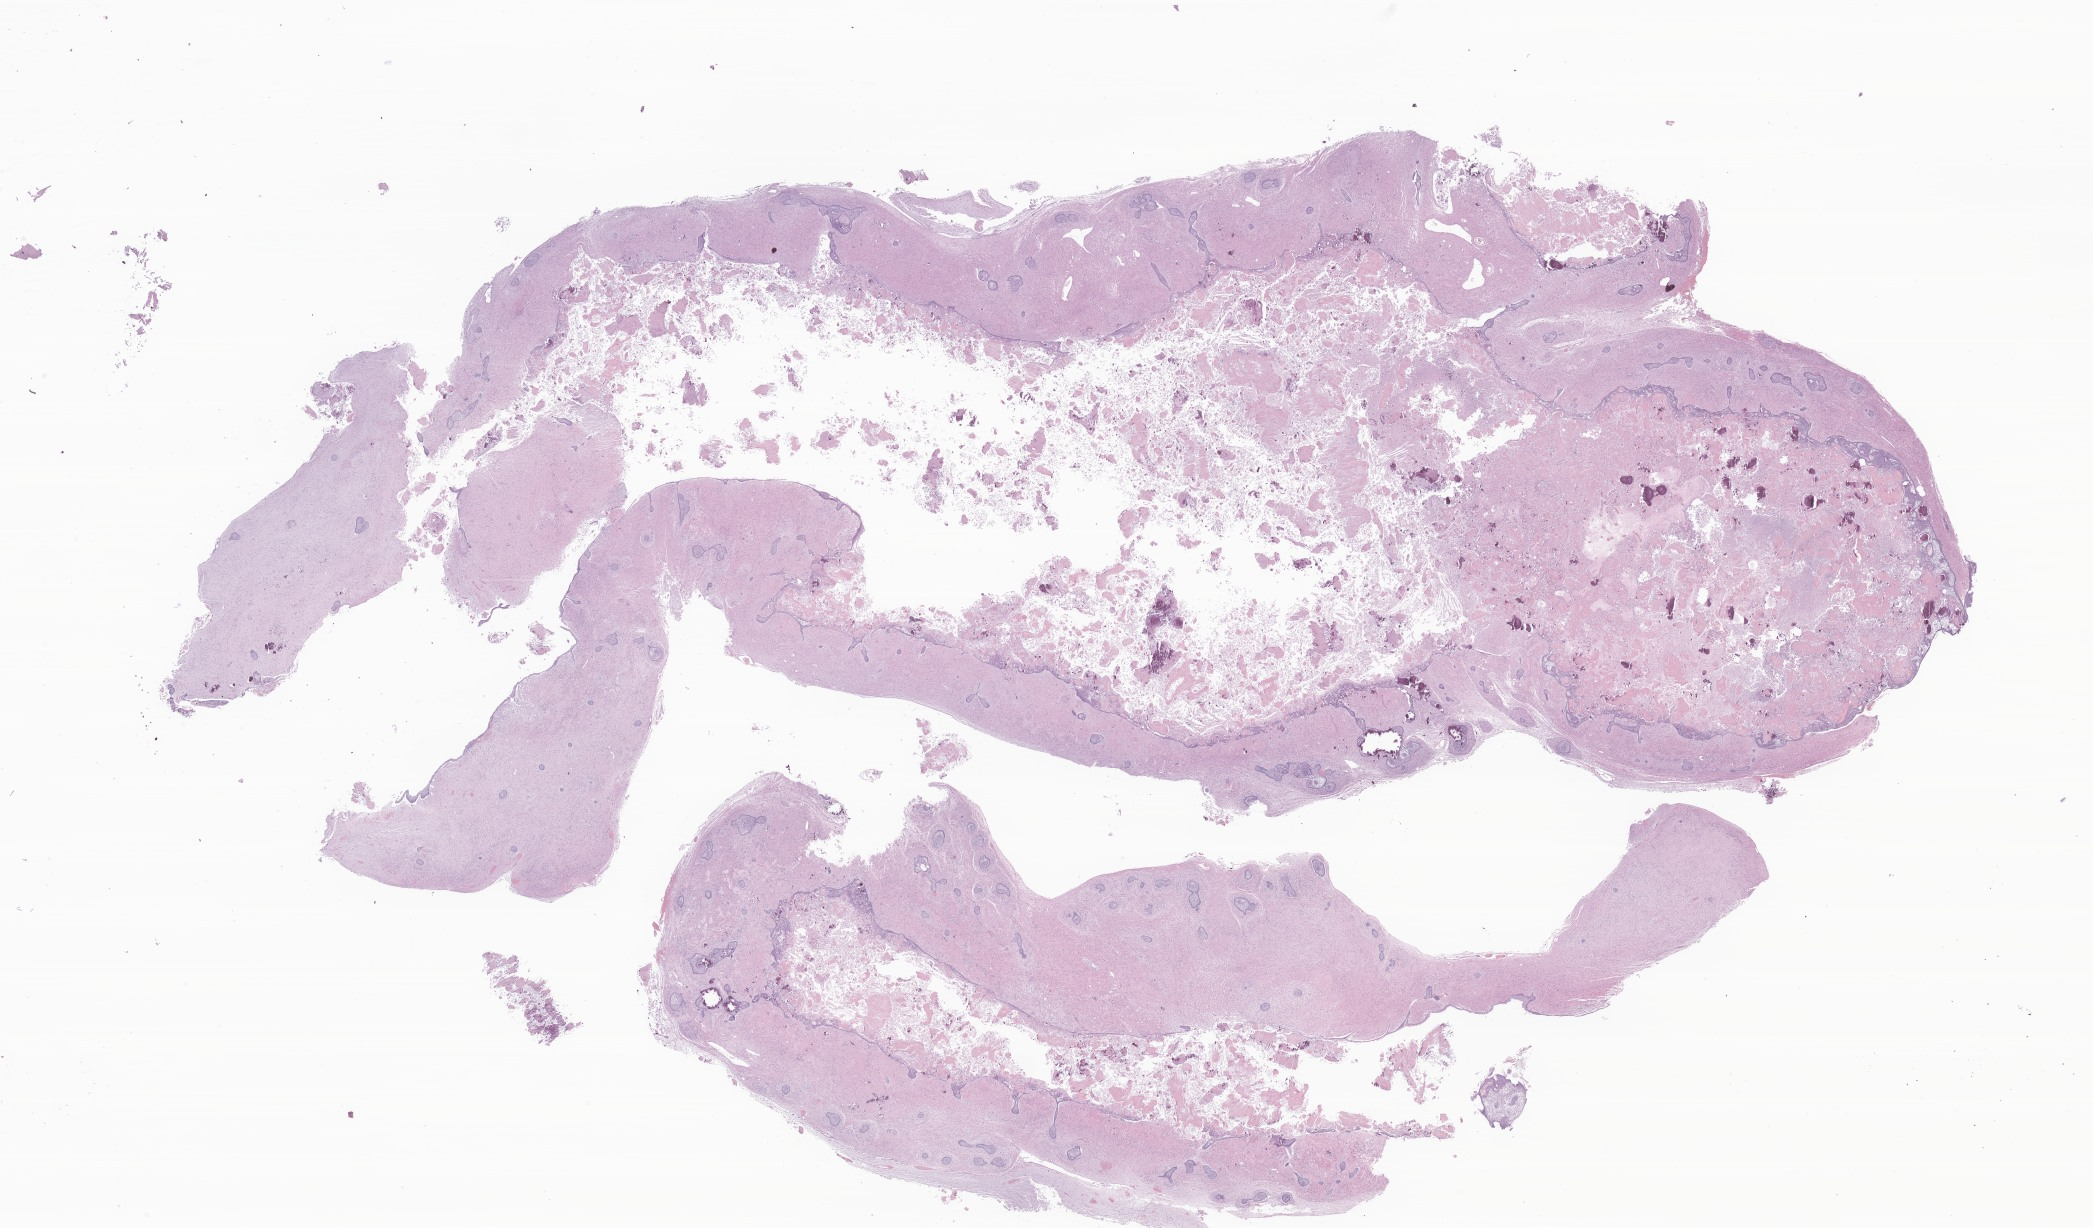
Whole-slide image, H&E stain of tumor tissue from the brain — whole scanned area (about 35.3 x 20.7 mm) shown as a low-resolution overview. Formalin-fixed, paraffin-embedded (FFPE) tissue. Patient: female, age 133 months (11 years 1 month).
* diagnosis: Craniopharyngioma, adamantinomatous